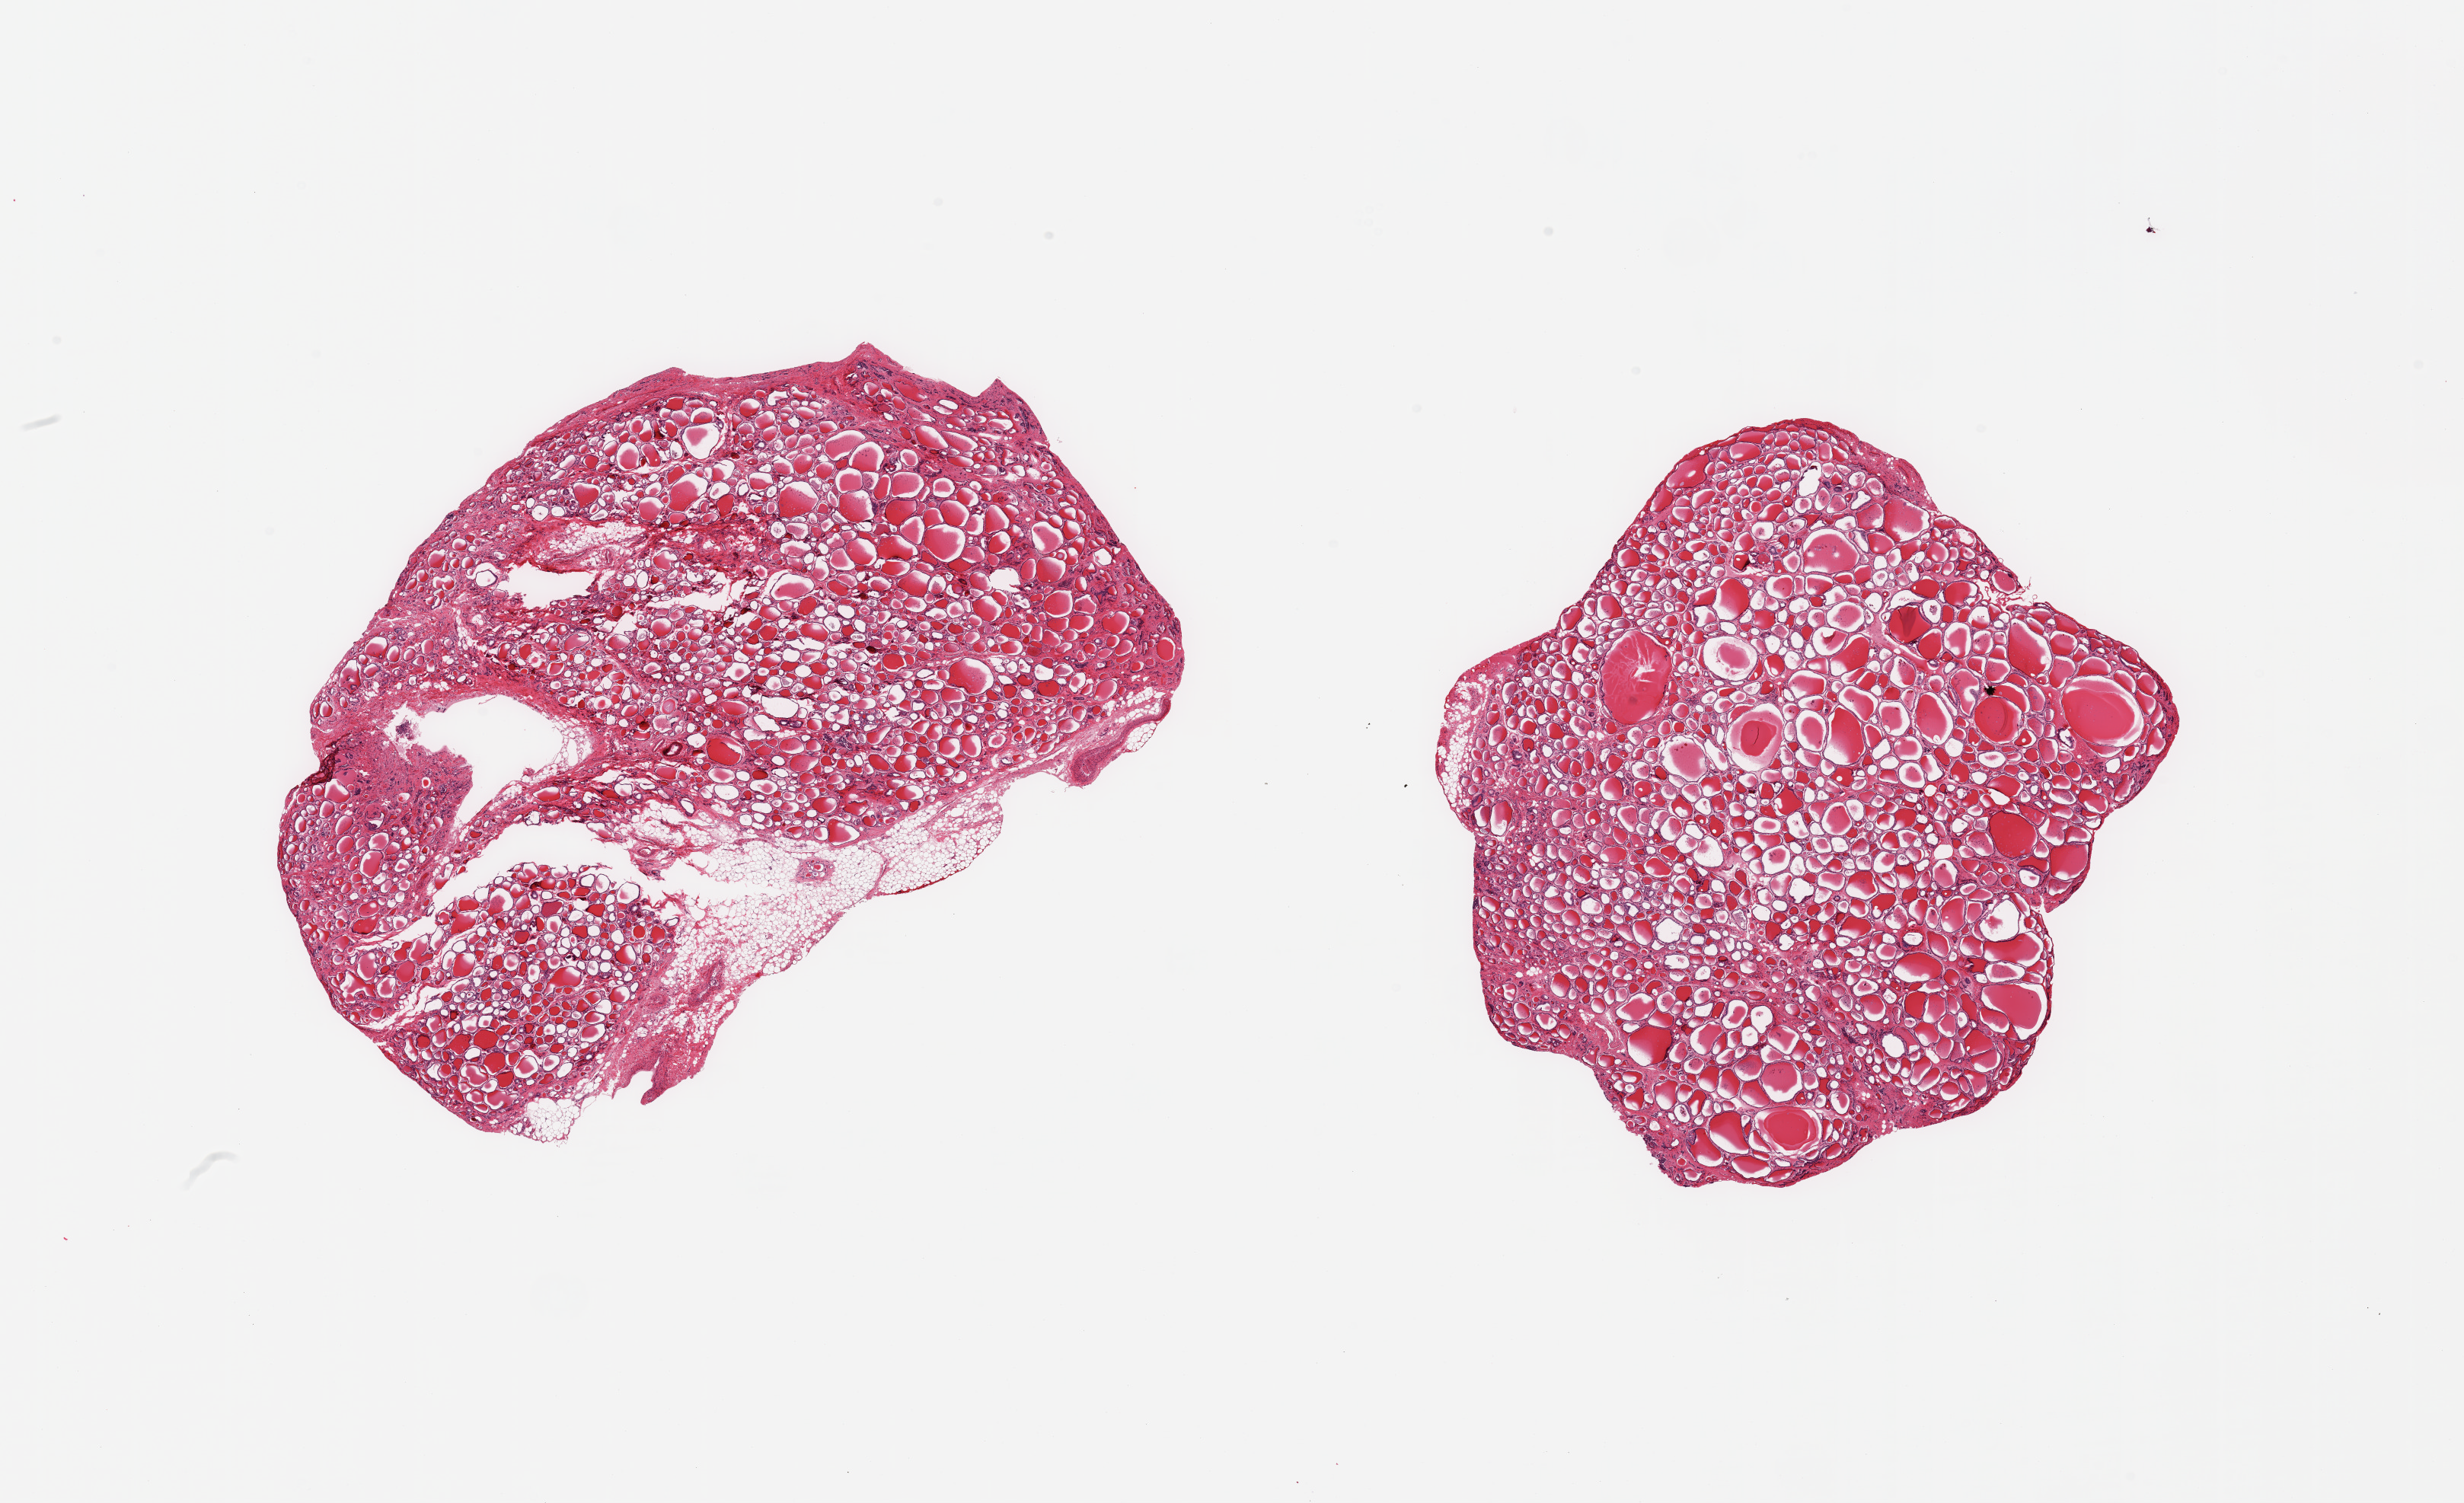
Digitized H&E-stained section — low-resolution overview of the scanned area, about 25.6 x 15.6 mm (acquisition: 20x scan); PAXgene-fixed paraffin-embedded (PFPE) section; target tissue: thyroid; donor tissue sample. Male donor.
Pathologist's review note for this sample: 2 pieces; 10% external fat on 1 piece.